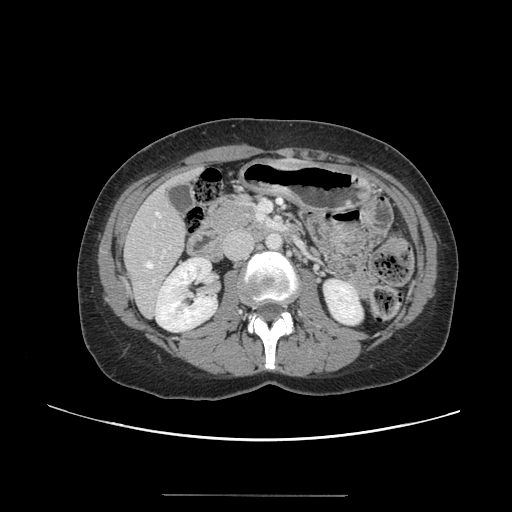
Contrast-enhanced abdominal CT, one axial slice. Position 51 of 144 along the scan axis. 120 kVp. Soft-tissue window (W 400 / L 40 HU). 2.5 mm slice thickness. 512 × 512 image matrix, field of view 380 × 380 mm. Female patient, age 53 years. From the clinical record (not read from this slice): diagnosis: colorectal cancer liver metastases, imaged before liver resection; multiple liver metastases: yes; largest metastasis: 1.1 cm; chemotherapy before resection: no.
Annotated regions visible in this slice (expert manual segmentation):
- hepatic veins: bounding box <147,212,160,268> (left, top, right, bottom; pixels)
- liver: <126,169,201,316>
- planned liver remnant (the part of the liver to remain after resection): <126,168,201,314>
- portal vein (with intrahepatic branches): <153,250,166,282>